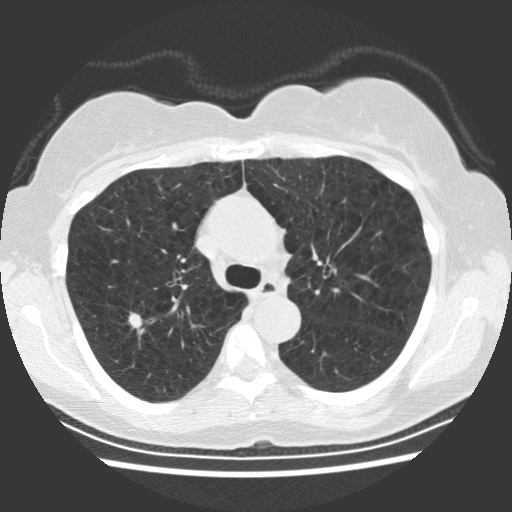
Low-dose screening chest CT, one axial slice. Position 163 of 234 along the scan axis. Reconstruction kernel STANDARD. Lung window (W 1500 / L -600 HU). 2.5 mm slice thickness. 512 × 512 image matrix, field of view 330 × 330 mm.
Annotated regions visible in this slice (manually delineated by an expert):
- lesion 1 (tumor, upper lobe of right lung): bounding box [x1, y1, x2, y2] px = [128, 313, 142, 329]